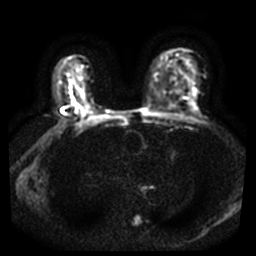
Breast MRI, one axial slice; slice 23 of 44 in the series (ordered by position); diffusion-weighted series; image 2 of 4 stored at this slice position (different b-values; order by instance number); 3 T; 5 mm slice thickness; 256 × 256 image matrix, field of view 340 × 340 mm. Female patient.
Outlined on this slice (outlined manually by an expert reader):
- tumour on diffusion-weighted imaging: bounding box [x1, y1, x2, y2] px = [70, 96, 77, 105]